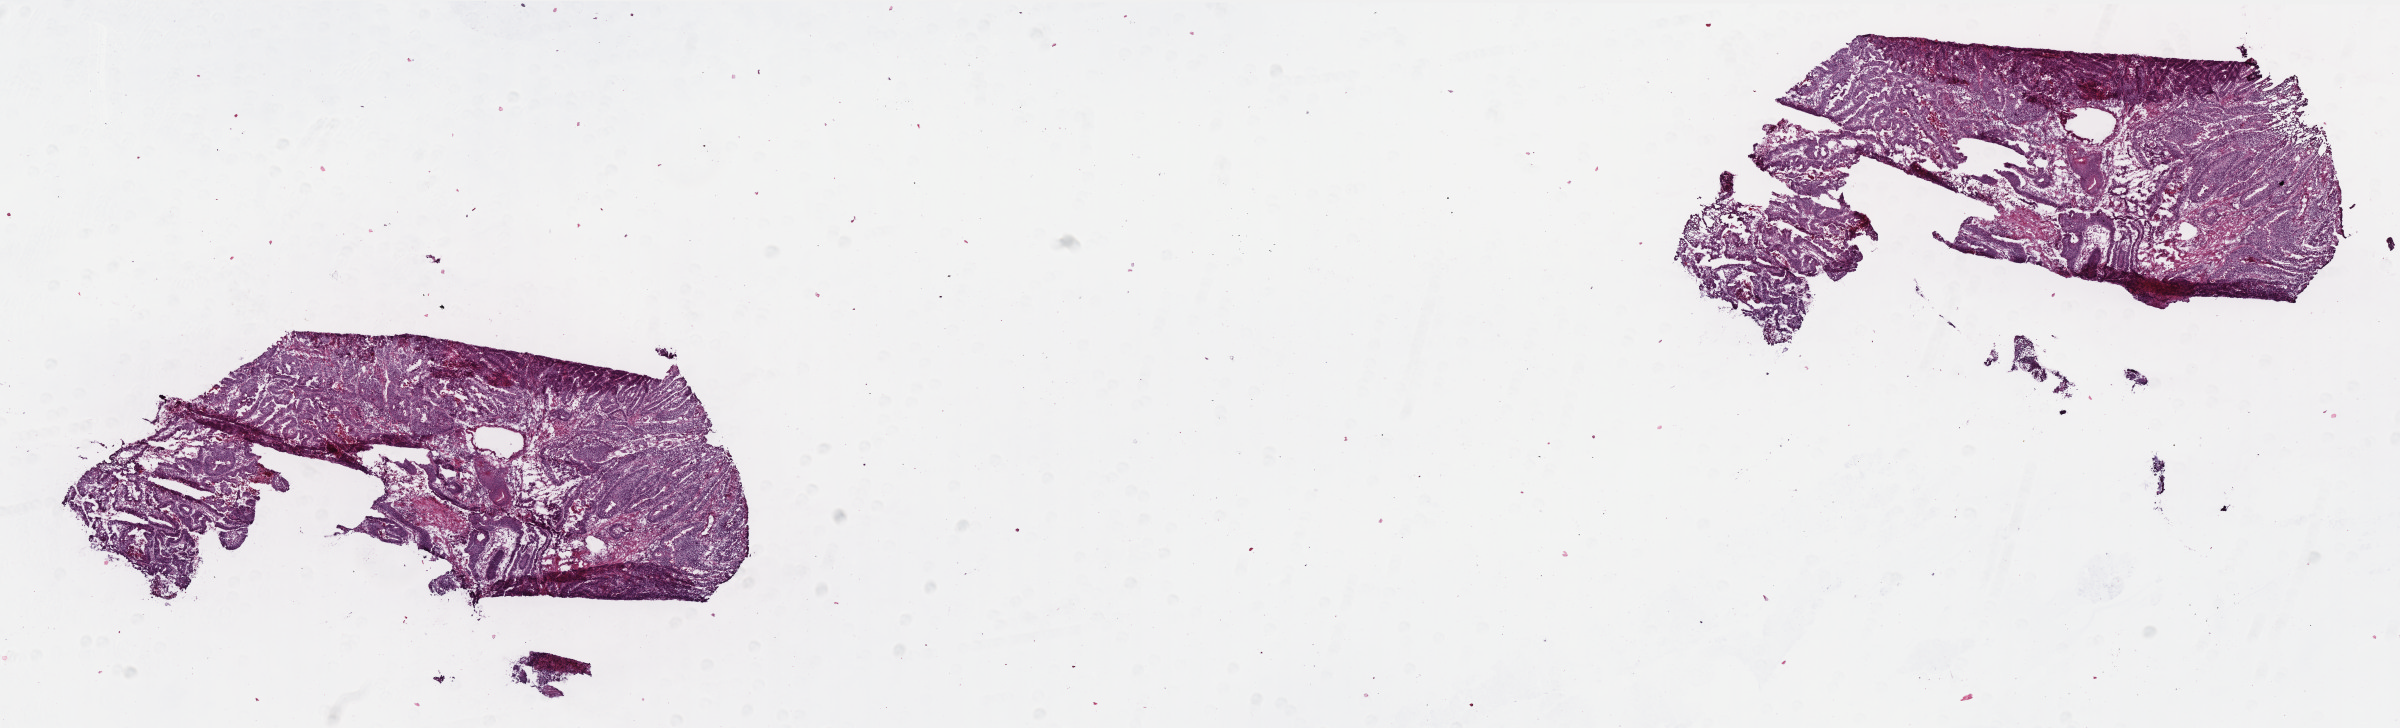
H&E whole-slide image — shown as a low-resolution overview of the whole scanned area (about 19.2 x 5.8 mm, from a 40x scan), frozen section, sample: primary tumour, colon. Patient: male, age at initial diagnosis 66 years. Pathologist review of this section (percent, as recorded): tumour cells 95%, tumour nuclei 80%, normal cells 0%, stromal cells 4%, necrosis 1%. Inflammatory infiltration, as recorded: lymphocyte infiltration 10%, monocyte infiltration 3%, neutrophil infiltration 4%.
Lymph nodes positive (case pathology): 0 of 32 examined. TNM: T3 N0 M0. Histologic diagnosis: Adenocarcinoma, NOS (transverse colon). AJCC pathologic stage: IIA (6th edition).